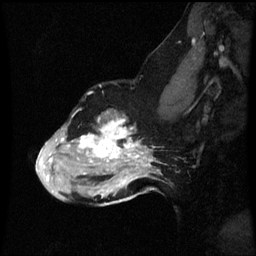
Breast MRI (dynamic contrast-enhanced), one sagittal slice; slice 41 of 60 in the series (ordered by position); dynamic contrast-enhanced series, image 2 of 3 at this slice position (ordered by acquisition); 1.5 T; TE 4.2 ms, TR 8.9 ms; 2 mm slice thickness; 256 × 256 image matrix, field of view 200 × 200 mm. Patient: female, 49 years. From the clinical record (not read from this slice): setting: breast cancer imaged before/during neoadjuvant chemotherapy; receptor status: HR-positive, HER2-negative.
Annotated regions visible in this slice (semi-automatic segmentation, software-assisted and operator-edited):
- analysis volume of interest (the breast-tissue region the enhancement analysis was run in; not a lesion): bounding box [x1, y1, x2, y2] px = [38, 110, 159, 199]
- tumour enhancement mask (voxels above the 70 % enhancement threshold inside the analysis volume of interest): [48, 118, 153, 181]